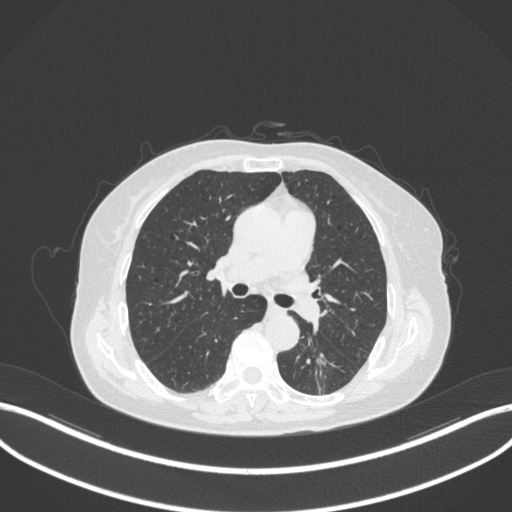
Chest CT, one axial slice. Slice 173 of 352 in the series (ordered by position). Reconstruction kernel B31f. Lung window (W 1500 / L -600 HU). 512 × 512 image matrix, field of view 400 × 400 mm. Female patient, age 70 years. Case-level facts recorded for this patient, not image findings: clinical TNM (as recorded): T1c N0 M0.
Structures marked on this image (rectangle marked by the reading radiologist):
- lung tumour (recorded histology: adenocarcinoma): box from (x=314, y=351) to (x=332, y=391) px